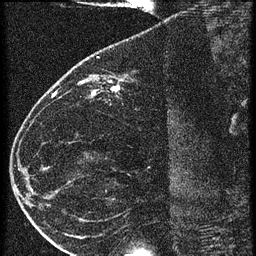
Breast MRI (dynamic contrast-enhanced), one sagittal slice; 3 images stored at this slice position (order not interpretable as contrast timing); 1.5 T; TE 4.2 ms, TR 20.4 ms; 1.5 mm slice thickness; 256 × 256 image matrix. Patient: female, 35 years. Case-level facts recorded for this patient, not image findings: setting: breast cancer imaged before/during neoadjuvant chemotherapy; receptor status: HR-positive, HER2-negative.
Outlined on this slice (semi-automatic segmentation, software-assisted and operator-edited):
- analysis volume of interest (the breast-tissue region the enhancement analysis was run in; not a lesion): bounding box <65,60,169,119> (left, top, right, bottom; pixels)
- tumour enhancement mask (voxels above the 90 % enhancement threshold inside the analysis volume of interest): <87,80,122,97>